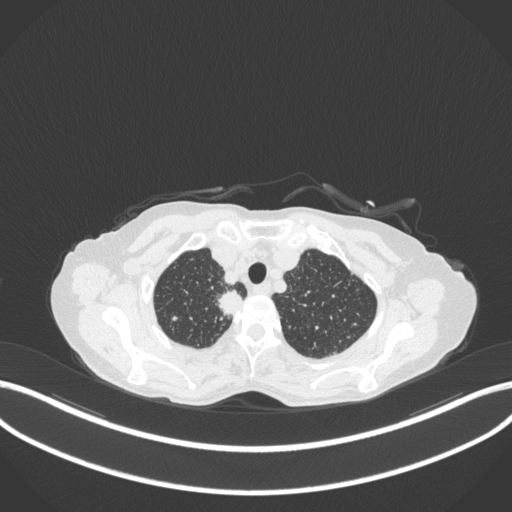
Chest CT, one axial slice; reconstruction kernel B31f; lung window (W 1500 / L -600 HU); 1 mm slice thickness; 512 × 512 image matrix, field of view 400 × 400 mm. Patient: female, 75 years. From the clinical record (not read from this slice): clinical TNM (as recorded): T1c N1 M1.
Outlined on this slice (bounding box drawn by a radiologist):
- lung tumour (recorded histology: adenocarcinoma): box from (x=214, y=292) to (x=248, y=320) px